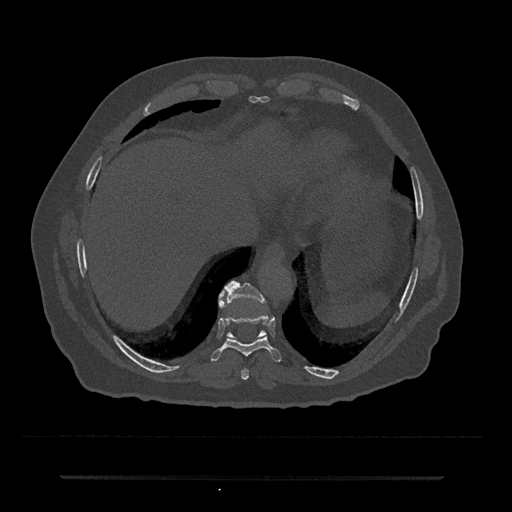
CT including the spine, one axial slice. Position 269 of 797 along the scan axis. 120 kVp. Bone window (W 1800 / L 400 HU). 0.5 mm slice thickness. 512 × 512 image matrix. Patient: male, 69 years. Case-level facts recorded for this patient, not image findings: primary cancer: prostate.
Annotated regions visible in this slice (semi-automatically segmented with operator editing):
- T10 vertebra: bounding box <219,281,266,339> (left, top, right, bottom; pixels)
- T8 vertebra: <241,368,249,380>
- T9 vertebra: <211,291,282,362>